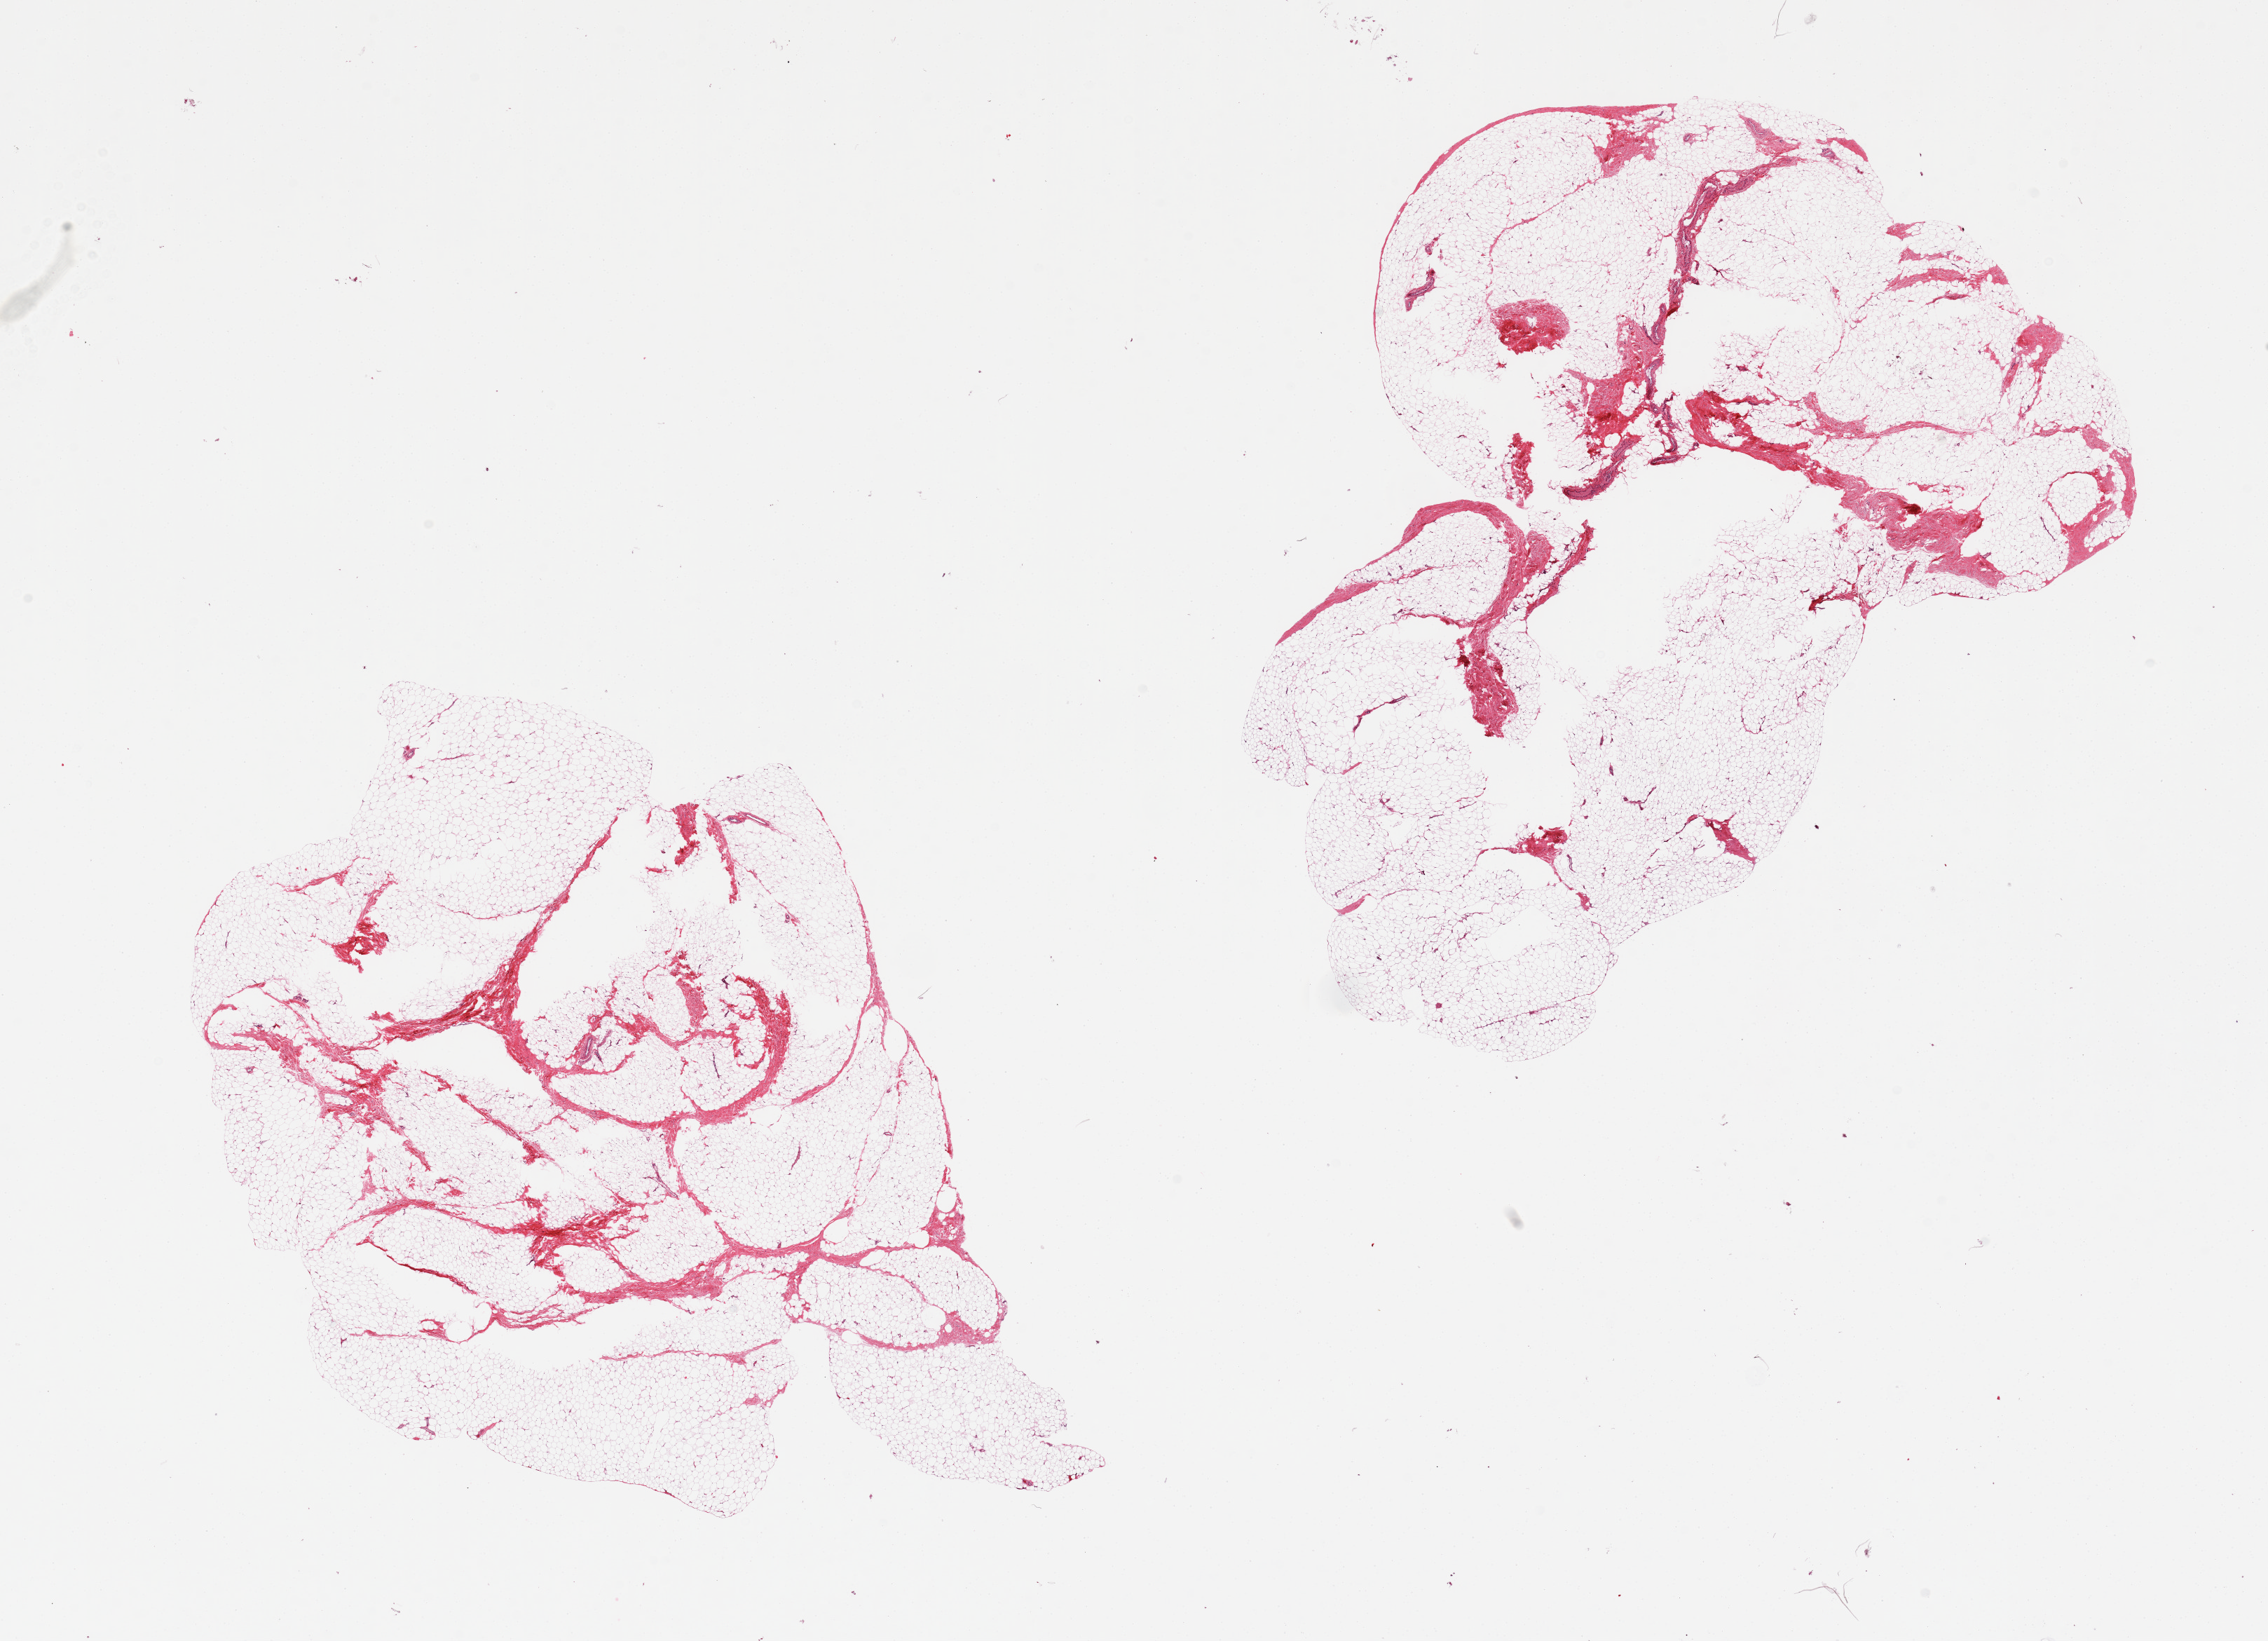
Haematoxylin and eosin whole-slide image — low-resolution overview of the scanned area, about 25.6 x 18.5 mm. PAXgene-fixed, paraffin-embedded tissue. Section of breast (target tissue). Donor tissue sample.
Reviewer comment on this tissue sample: 2 pieces, predominantly adipose tissue with limited fibrous stroma and no ductal elements identified.